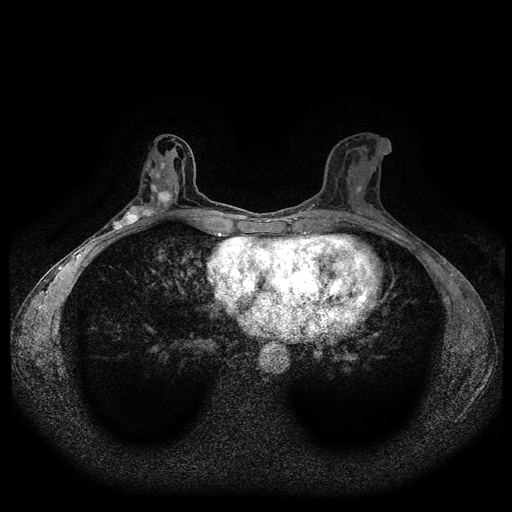
Breast MRI (dynamic contrast-enhanced, multi-phase), one axial slice. Slice 49 of 116 in the series (ordered by position). Dynamic contrast-enhanced series, time point 2 of 5 at this slice position (early post-contrast). 1.5 T. TE 2.6 ms, TR 5.3 ms. 2 mm slice thickness. 512 × 512 image matrix. Female patient, age 50 years.
Outlined on this slice (semi-automatically segmented with operator editing):
- breast lesion (labelled 'tumour' in the annotation; benign lesions carry a separate 'benign' label): bounding box <110,183,173,234> (left, top, right, bottom; pixels)